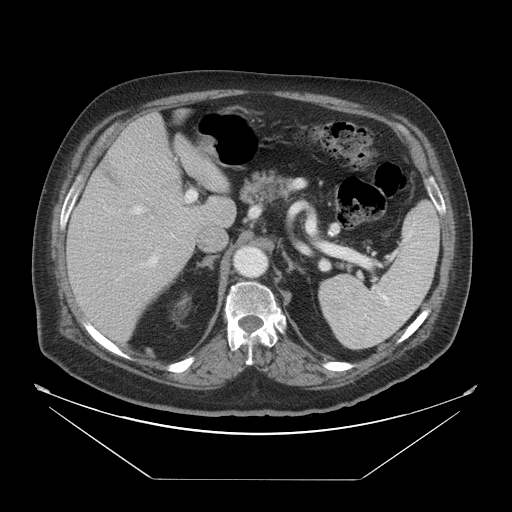
Contrast-enhanced abdominal CT, one axial slice. Slice 32 of 45 in the series (ordered by position). Intravenous contrast given. Soft-tissue window (W 400 / L 40 HU). 5 mm slice thickness. 512 × 512 image matrix, field of view 463 × 463 mm. Male patient, age 87 years. From the clinical record (not read from this slice): diagnosis: colorectal cancer liver metastases, imaged before liver resection; multiple liver metastases: no; largest metastasis: 4.5 cm.
Structures marked on this image (outlined manually by an expert reader):
- liver: bounding box (x1, y1, x2, y2) in pixels: (66, 113, 236, 343)
- planned liver remnant (the part of the liver to remain after resection): (119, 113, 226, 182)
- portal vein (with intrahepatic branches): (119, 159, 197, 267)
- liver metastasis: (139, 209, 157, 224)
- liver metastasis: (98, 153, 131, 192)